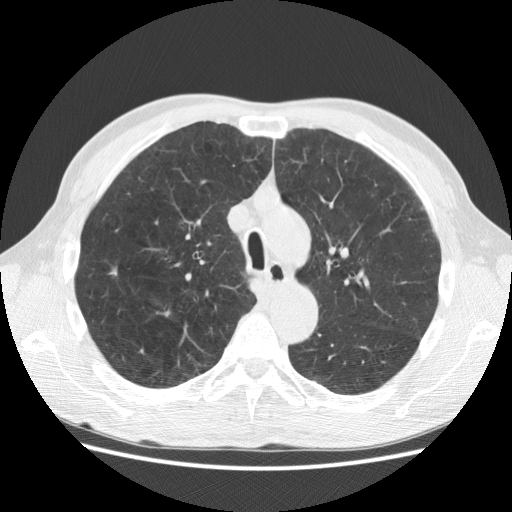
Axial slice from a low-dose chest CT screening exam, baseline annual screen, lung window (W 1500 / L -600 HU), standard (soft-tissue) reconstruction kernel (STANDARD). Male participant, aged 62 years at enrolment. Current smoker at enrolment.
Lesion marked by an expert reader, bounding box [x1, y1, x2, y2] px = [101, 260, 134, 291]. The screening reader recorded 2 non-calcified nodules or masses ≥4 mm on this exam (right upper lobe, left lower lobe); which of them this box marks is not recorded. Official screen result: positive, change unspecified: nodule(s) >= 4 mm or enlarging nodule(s), mass(es), or other non-specific abnormalities suspicious for lung cancer. Participant outcome: lung cancer diagnosed 183 days after this screen — bronchiolo-alveolar adenocarcinoma, NOS, right upper lobe, moderately differentiated (G2), stage IIA (AJCC 6th edition), 11 mm at pathology.